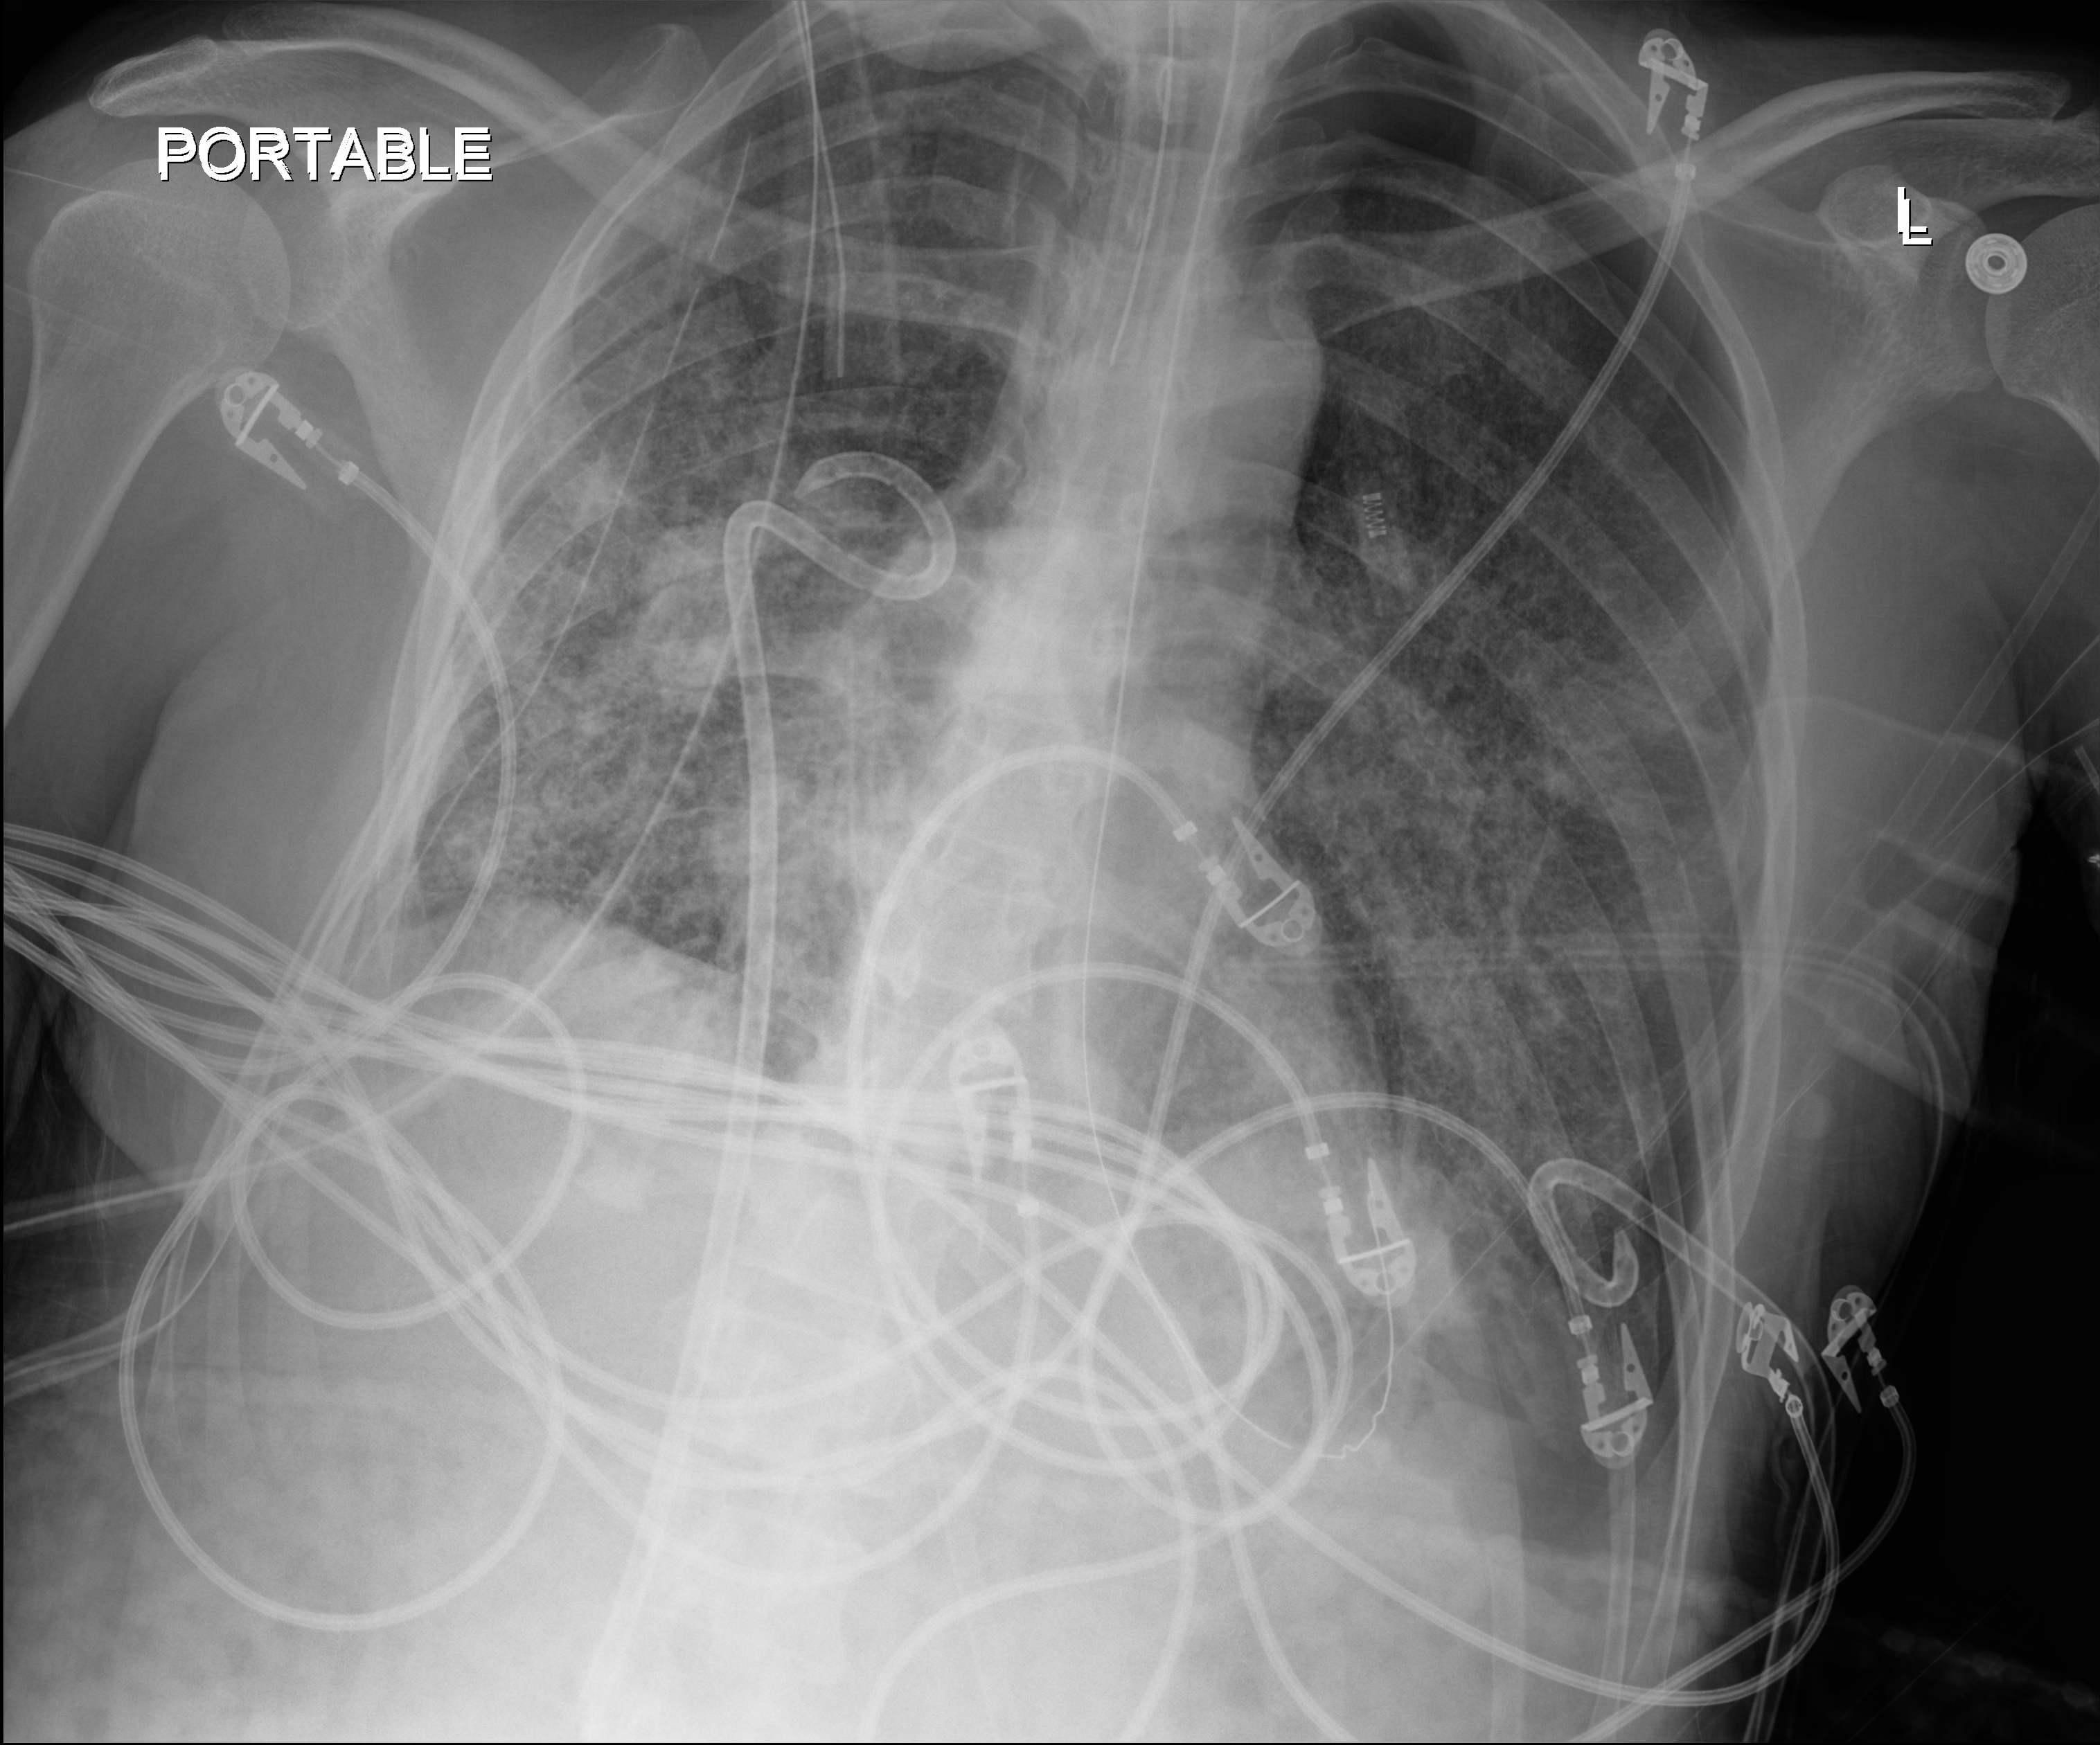
Chest radiograph, anteroposterior (AP) projection. Adult patient hospitalised with COVID-19, age 18–59 years.
Admission-level facts for this patient (not findings on this image; timing relative to this image not recorded):
- hypertension (admission record): no
- length of hospital stay: 41 days